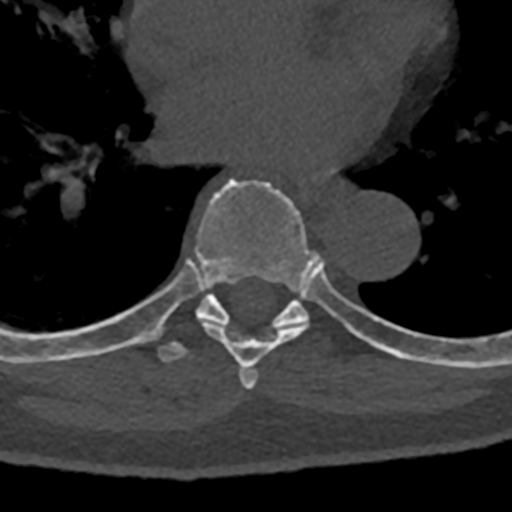
CT including the spine, one axial slice. Slice 742 of 797 in the series (ordered by position). 120 kVp. Bone window (W 1800 / L 400 HU). 512 × 512 image matrix. Male patient, age 74 years. Case-level facts recorded for this patient, not image findings: primary cancer: renal; vertebrae with lytic lesions (as recorded): T10, L1, L2, L3, L4, L5.
Structures marked on this image (semi-automatically segmented with operator editing):
- T6 vertebra: bounding box [x1, y1, x2, y2] px = [239, 368, 258, 385]
- T7 vertebra: [136, 179, 394, 389]
- T8 vertebra: [70, 293, 432, 364]